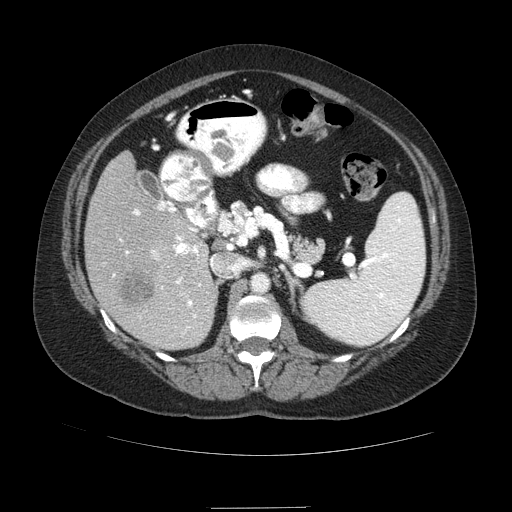
Contrast-enhanced abdominal CT (liver protocol), one axial slice. Position 43 of 89 along the scan axis. Reconstruction kernel STANDARD. 120 kVp. Soft-tissue window (W 400 / L 40 HU). 2.5 mm slice thickness. 512 × 512 image matrix. Case-level facts recorded for this patient, not image findings: diagnosis: hepatocellular carcinoma (patient treated with transarterial chemoembolisation; whether this scan precedes or follows treatment is not stated here); TNM stage (as recorded): Stage-IIIB; Child-Pugh class: A; tumour nodularity: multinodular.
Structures marked on this image (semi-automatically segmented with operator editing):
- liver parenchyma outside the tumour (the mass and vessels are separate outlines, so this box may not span the whole liver): bounding box (x1, y1, x2, y2) in pixels: (84, 152, 218, 349)
- mass: (117, 270, 153, 312)
- liver vessels: (113, 201, 201, 334)